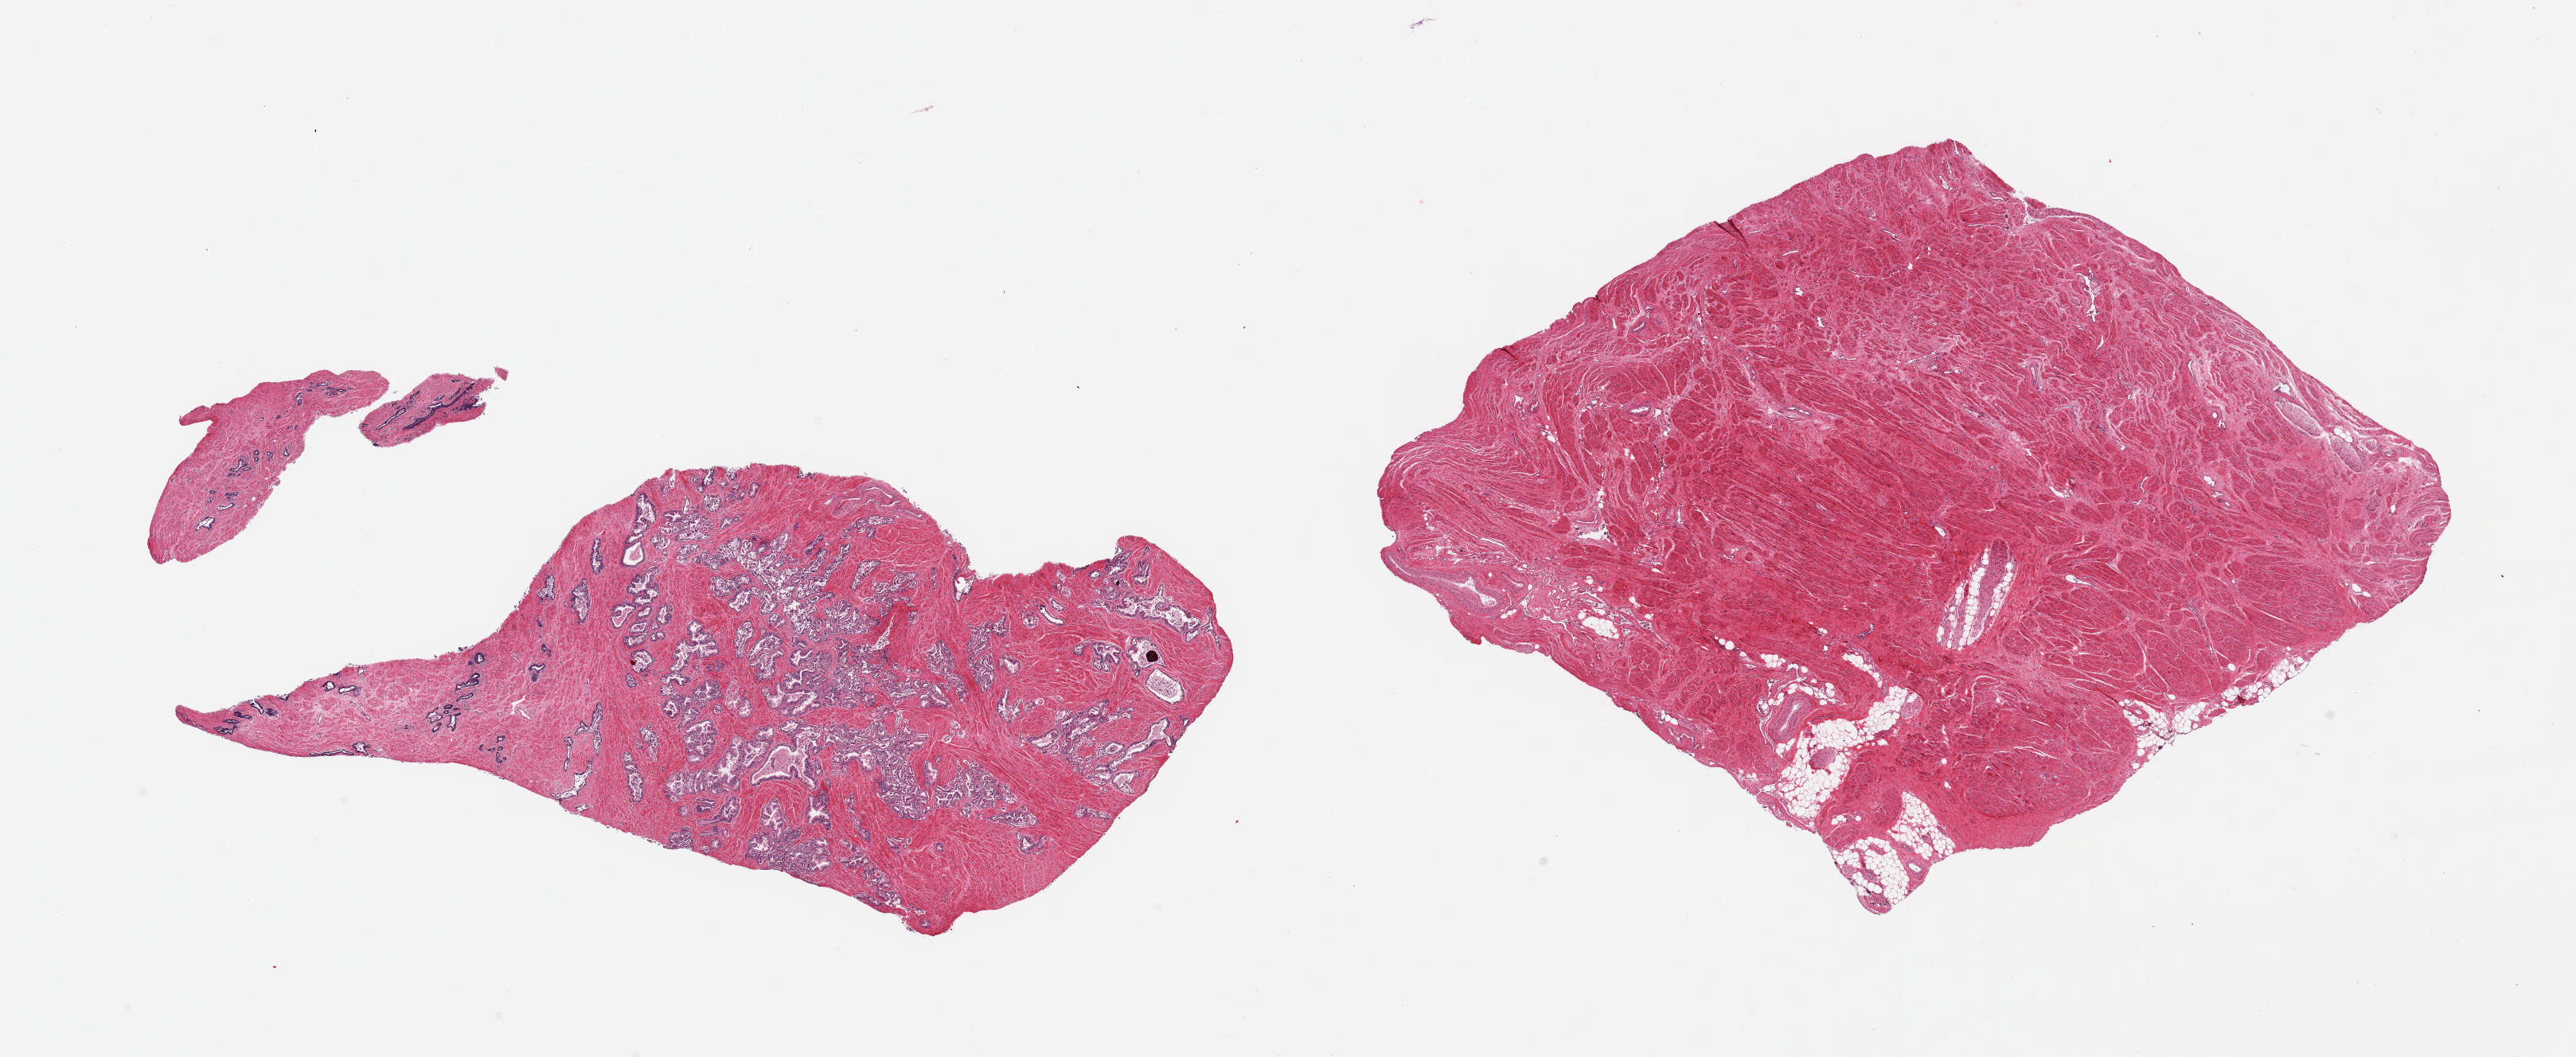
Hematoxylin and eosin (H&E) whole-slide image — low-resolution overview of the scanned area, about 25.6 x 10.5 mm (acquisition: 20x scan); PAXgene-fixed, paraffin-embedded tissue; target tissue: prostate; tissue donor sample.
Pathologist's review note for this sample: 2 pieces; 1 consists of fibromuscular stroma only and other is composed of tubuloalveolar glands embedded in fibromuscular stroma; two tiny separated prostatic tissue fragments.